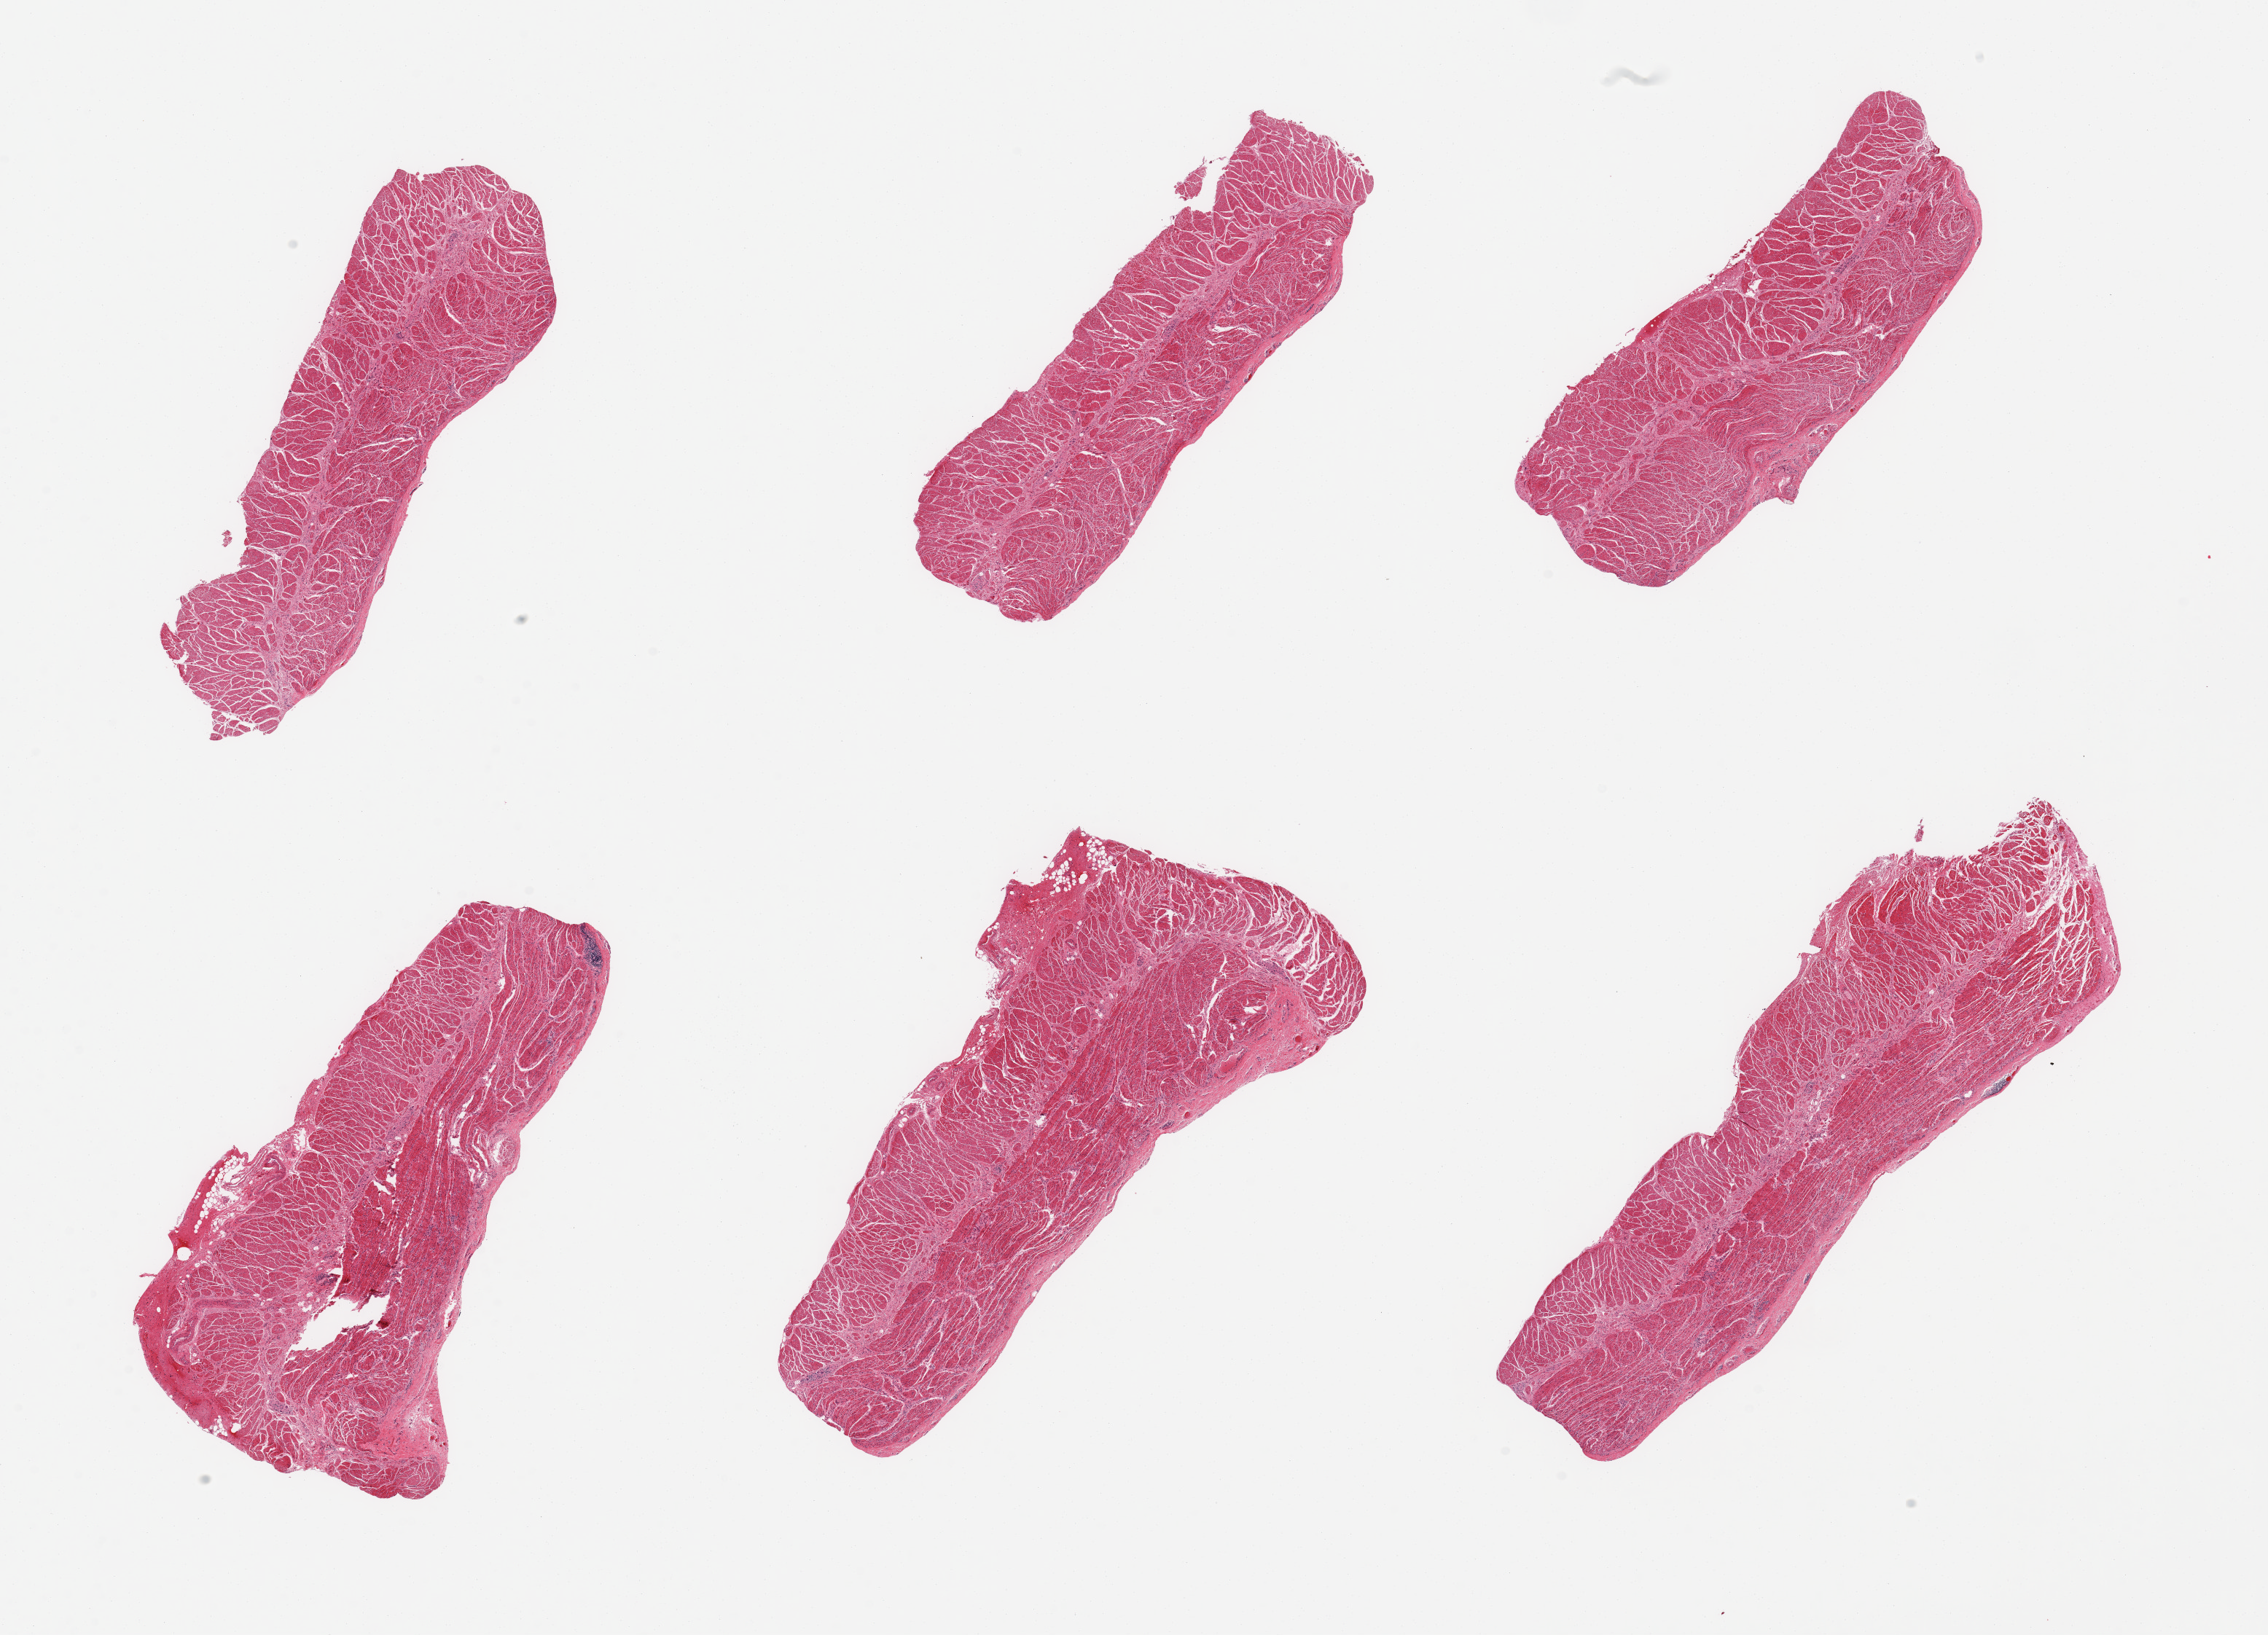
Digitized haematoxylin and eosin-stained section — a low-resolution overview of the entire scanned area, about 24.6 x 17.7 mm. PAXgene-fixed, paraffin-embedded tissue. Section of esophageal muscle (target tissue). Donor tissue sample. Donor: male.
Pathologist's review note for this sample: 6 pieces, confirmed target muscularis.